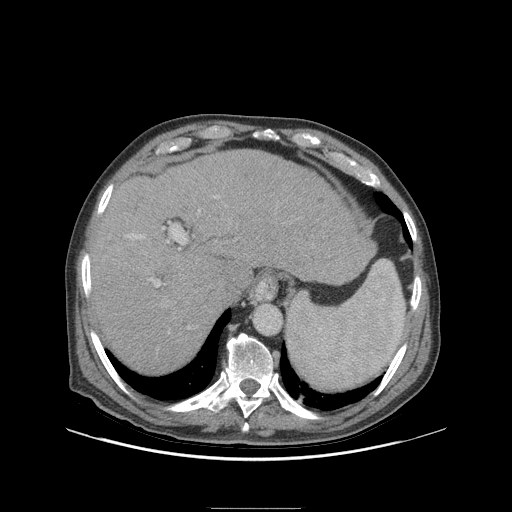
Contrast-enhanced abdominal CT (liver protocol), one axial slice; slice 76 of 105 in the series (ordered by position); reconstruction kernel STANDARD; 140 kVp; soft-tissue window (W 400 / L 40 HU); 512 × 512 image matrix. From the clinical record (not read from this slice): diagnosis: hepatocellular carcinoma (patient treated with transarterial chemoembolisation; whether this scan precedes or follows treatment is not stated here); TNM stage (as recorded): Stage-I; Child-Pugh class: A; tumour nodularity: uninodular; tumour size: 5.1 cm.
Structures marked on this image (semi-automatic segmentation, software-assisted and operator-edited):
- abdominal aorta: bounding box (x1, y1, x2, y2) in pixels: (254, 305, 282, 335)
- liver parenchyma outside the tumour (the mass and vessels are separate outlines, so this box may not span the whole liver): (90, 149, 372, 372)
- liver vessels: (126, 195, 219, 329)